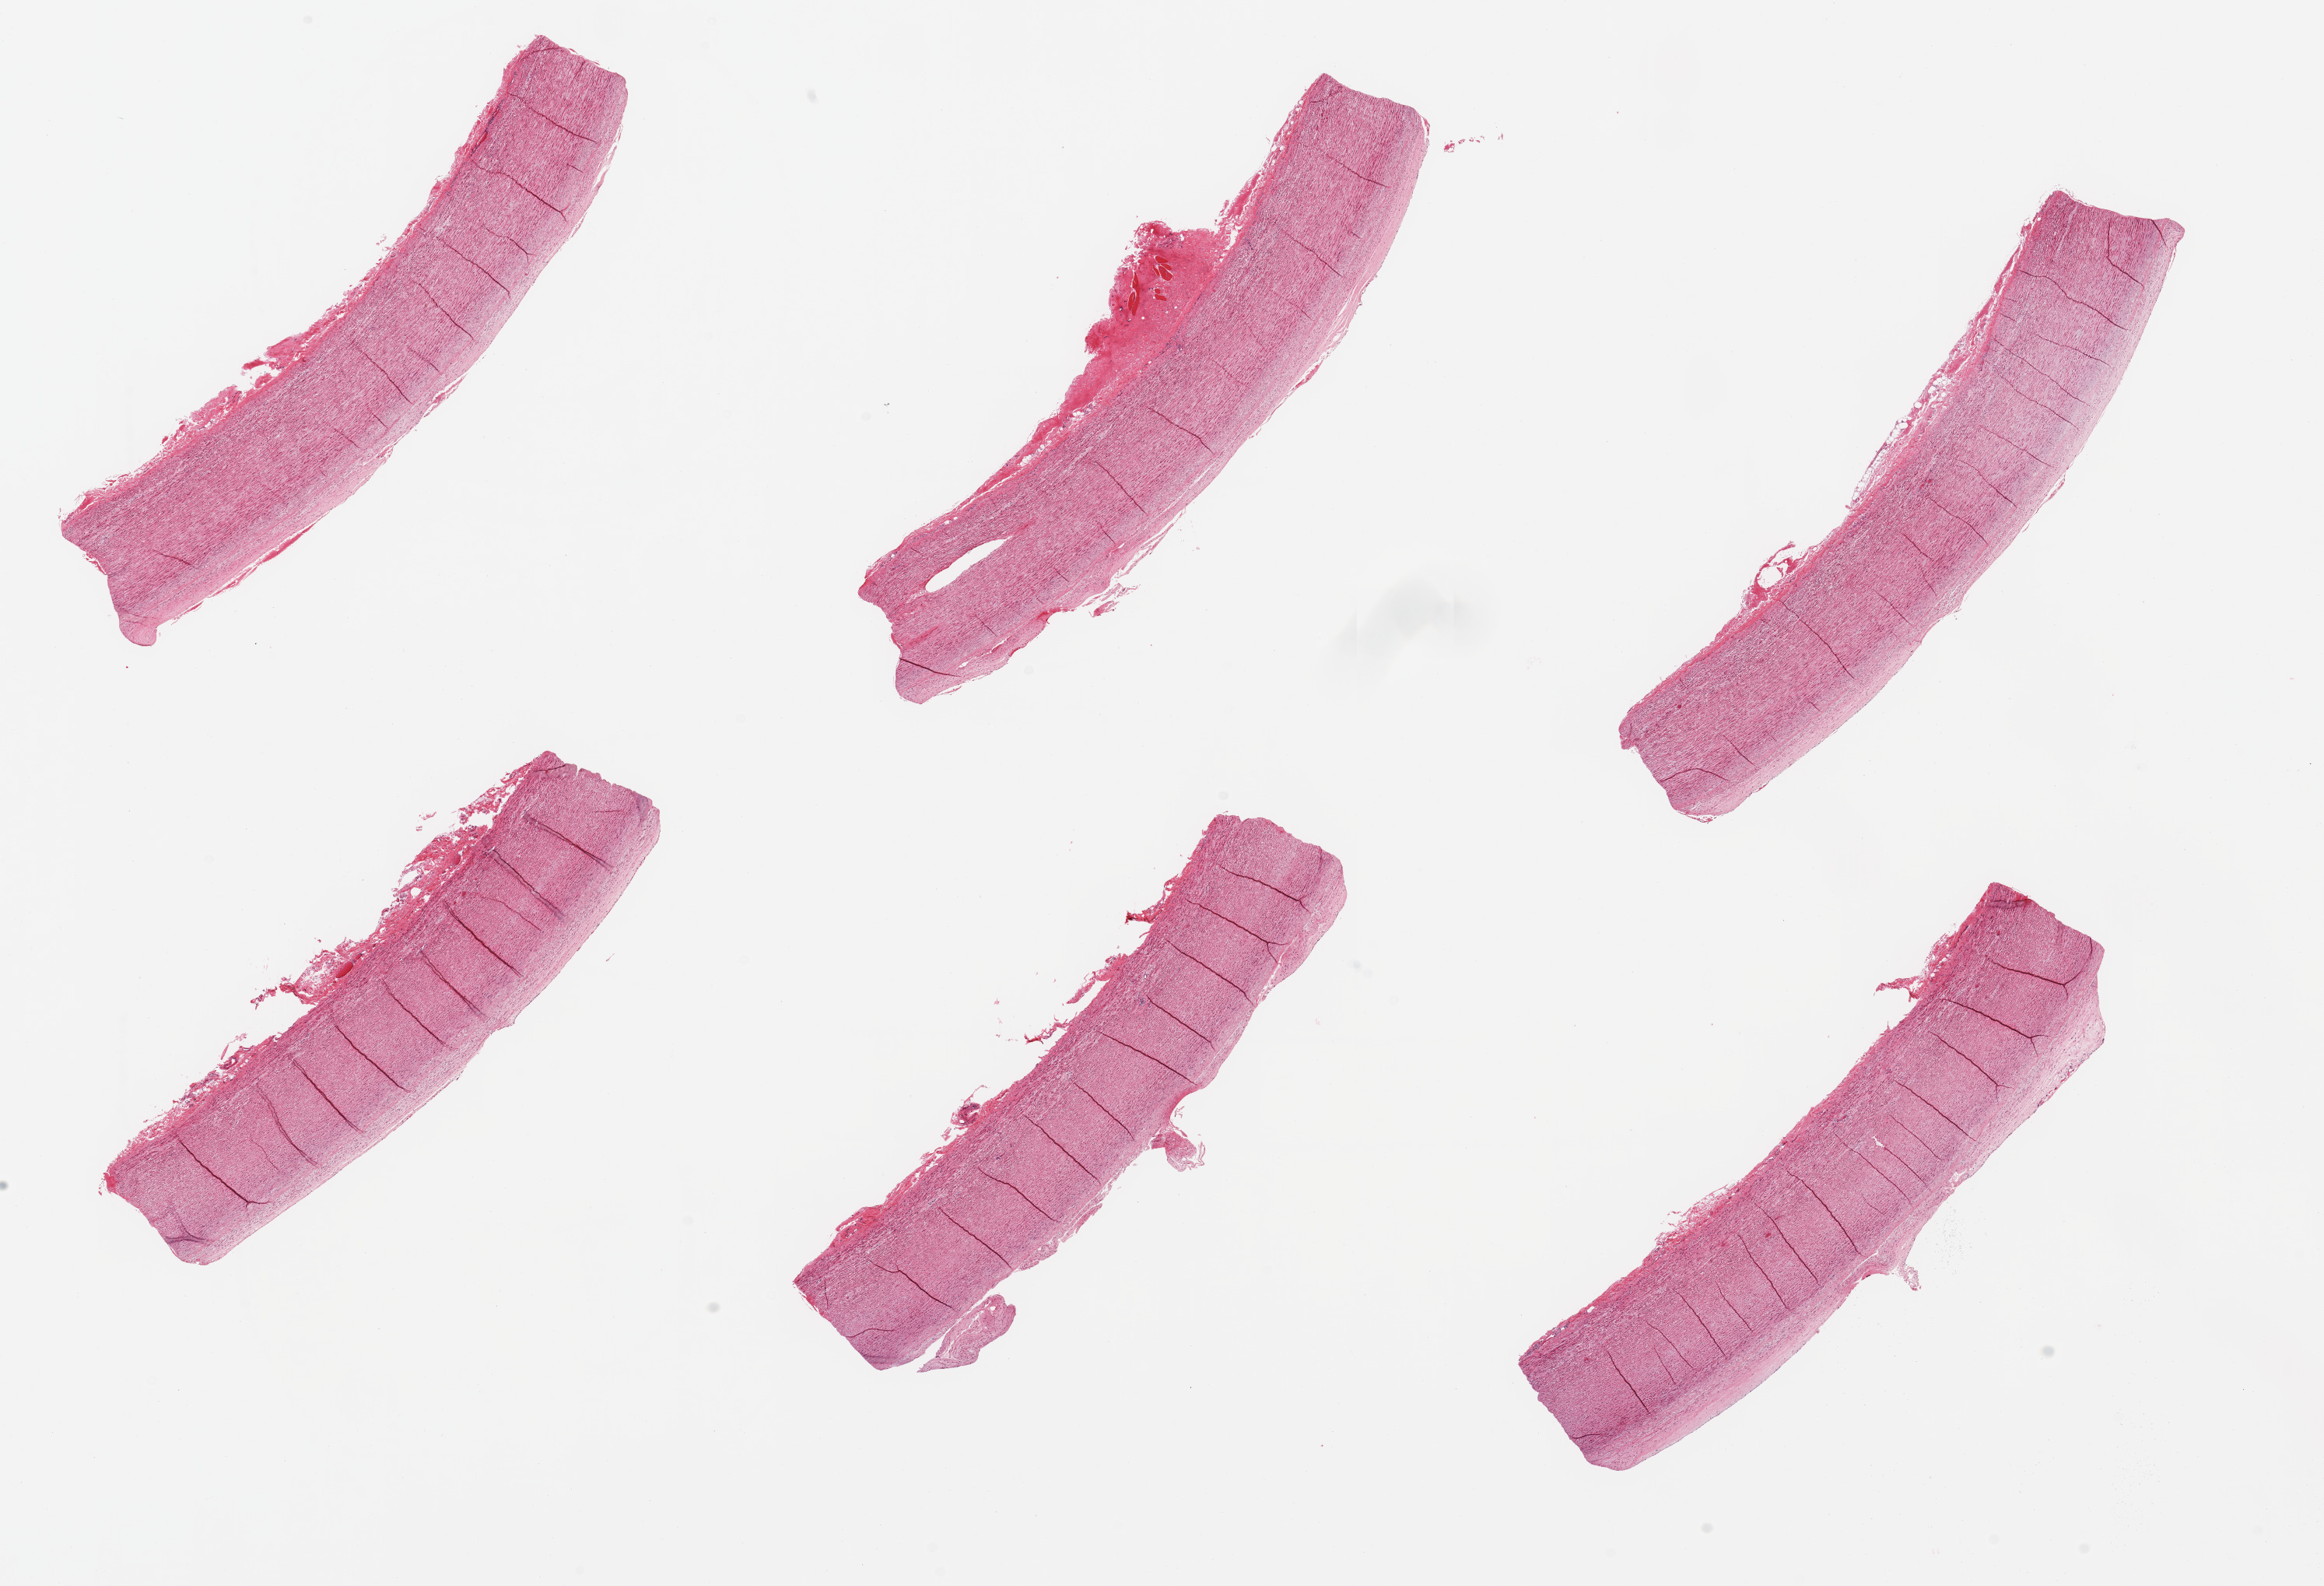
Hematoxylin and eosin (H&E) whole-slide image, brightfield, whole scanned area (about 23.6 x 16.1 mm, acquisition: 20x scan) shown as a low-resolution overview, PAXgene-fixed, paraffin-embedded tissue, target tissue: aorta, tissue donor sample. Donor: female.
Reviewer comment on this tissue sample: 6 pieces; small amount of plaque.